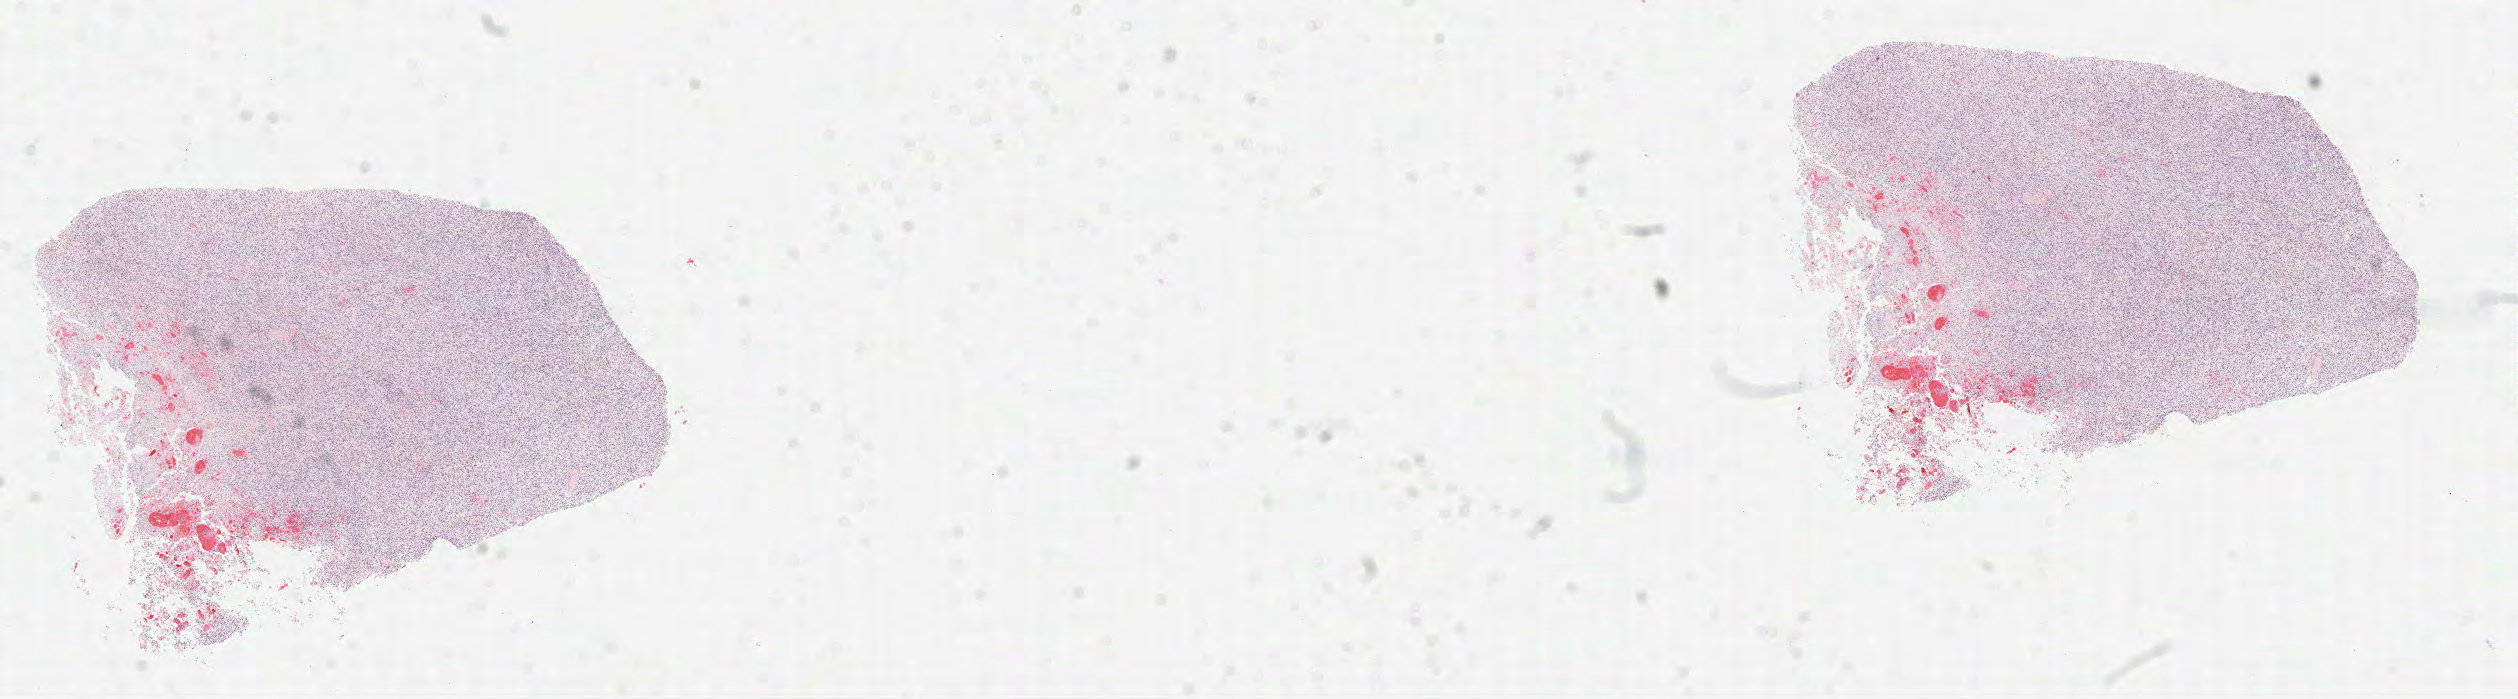
Digitized Hematoxylin and eosin (H&E) stained tissue section (whole slide), low-resolution overview of the scanned area, about 20.3 x 5.6 mm. Formalin-fixed paraffin-embedded (FFPE) diagnostic section. Primary tumour sample from the brain. Female, age 74 years at initial diagnosis.
• histologic diagnosis: Glioblastoma